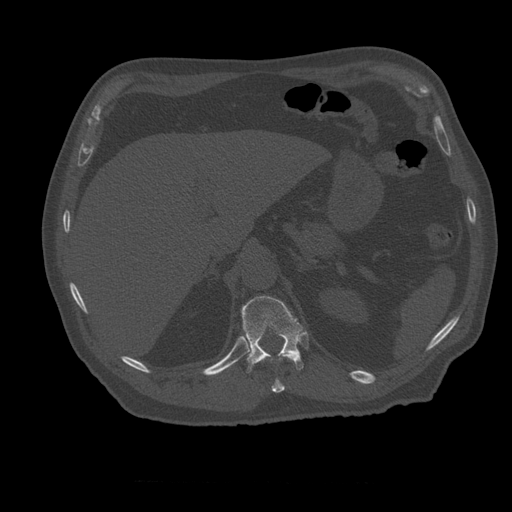
CT including the spine, one axial slice. Position 265 of 399 along the scan axis. Reconstruction kernel STANDARD. 120 kVp. Bone window (W 1800 / L 400 HU). 1.25 mm slice thickness. 512 × 512 image matrix, field of view 407 × 407 mm. Patient age 73 years. From the clinical record (not read from this slice): primary cancer: prostate.
Structures marked on this image (semi-automatically segmented with operator editing):
- T11 vertebra: bounding box [x1, y1, x2, y2] px = [259, 354, 298, 393]
- T12 vertebra: [241, 296, 304, 373]